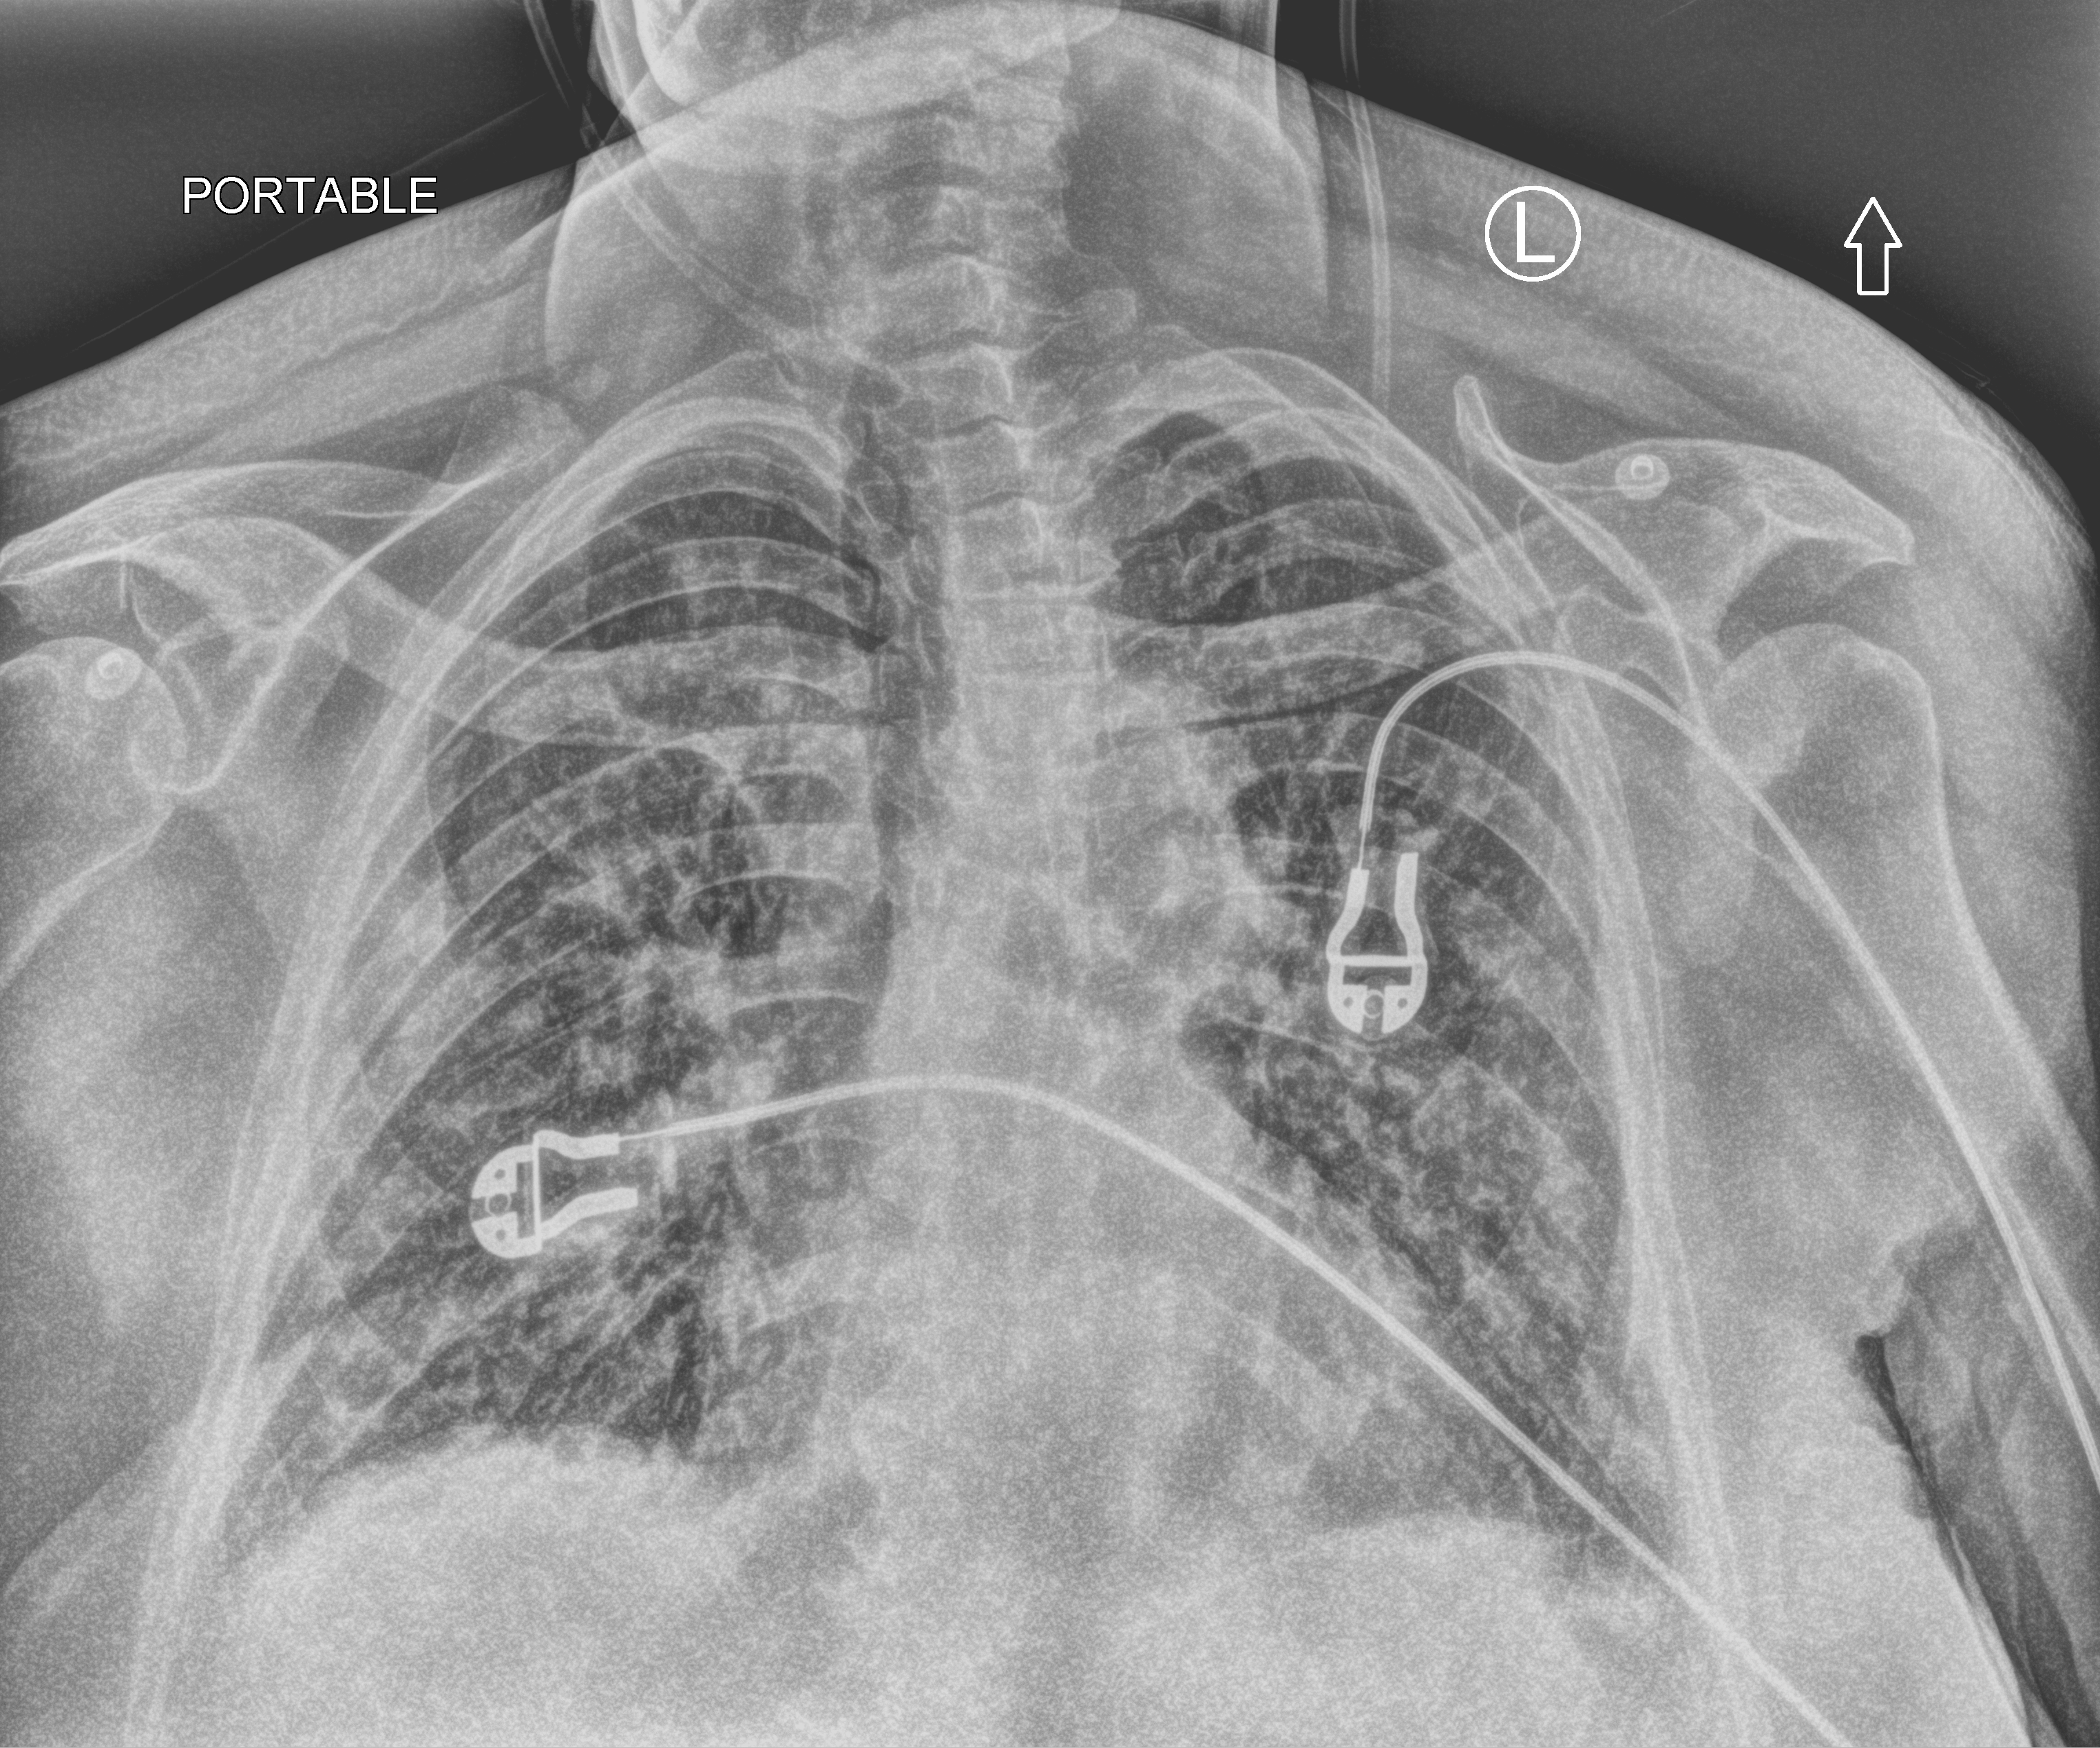
Chest X-ray (portable); anteroposterior (AP) projection. Patient hospitalised with COVID-19; female, aged 60–74 years.
Hospital-stay facts (about this admission, not read from this image; timing relative to this image not recorded): admitted to intensive care during this hospital stay: no; mechanically ventilated during this hospital stay: no.